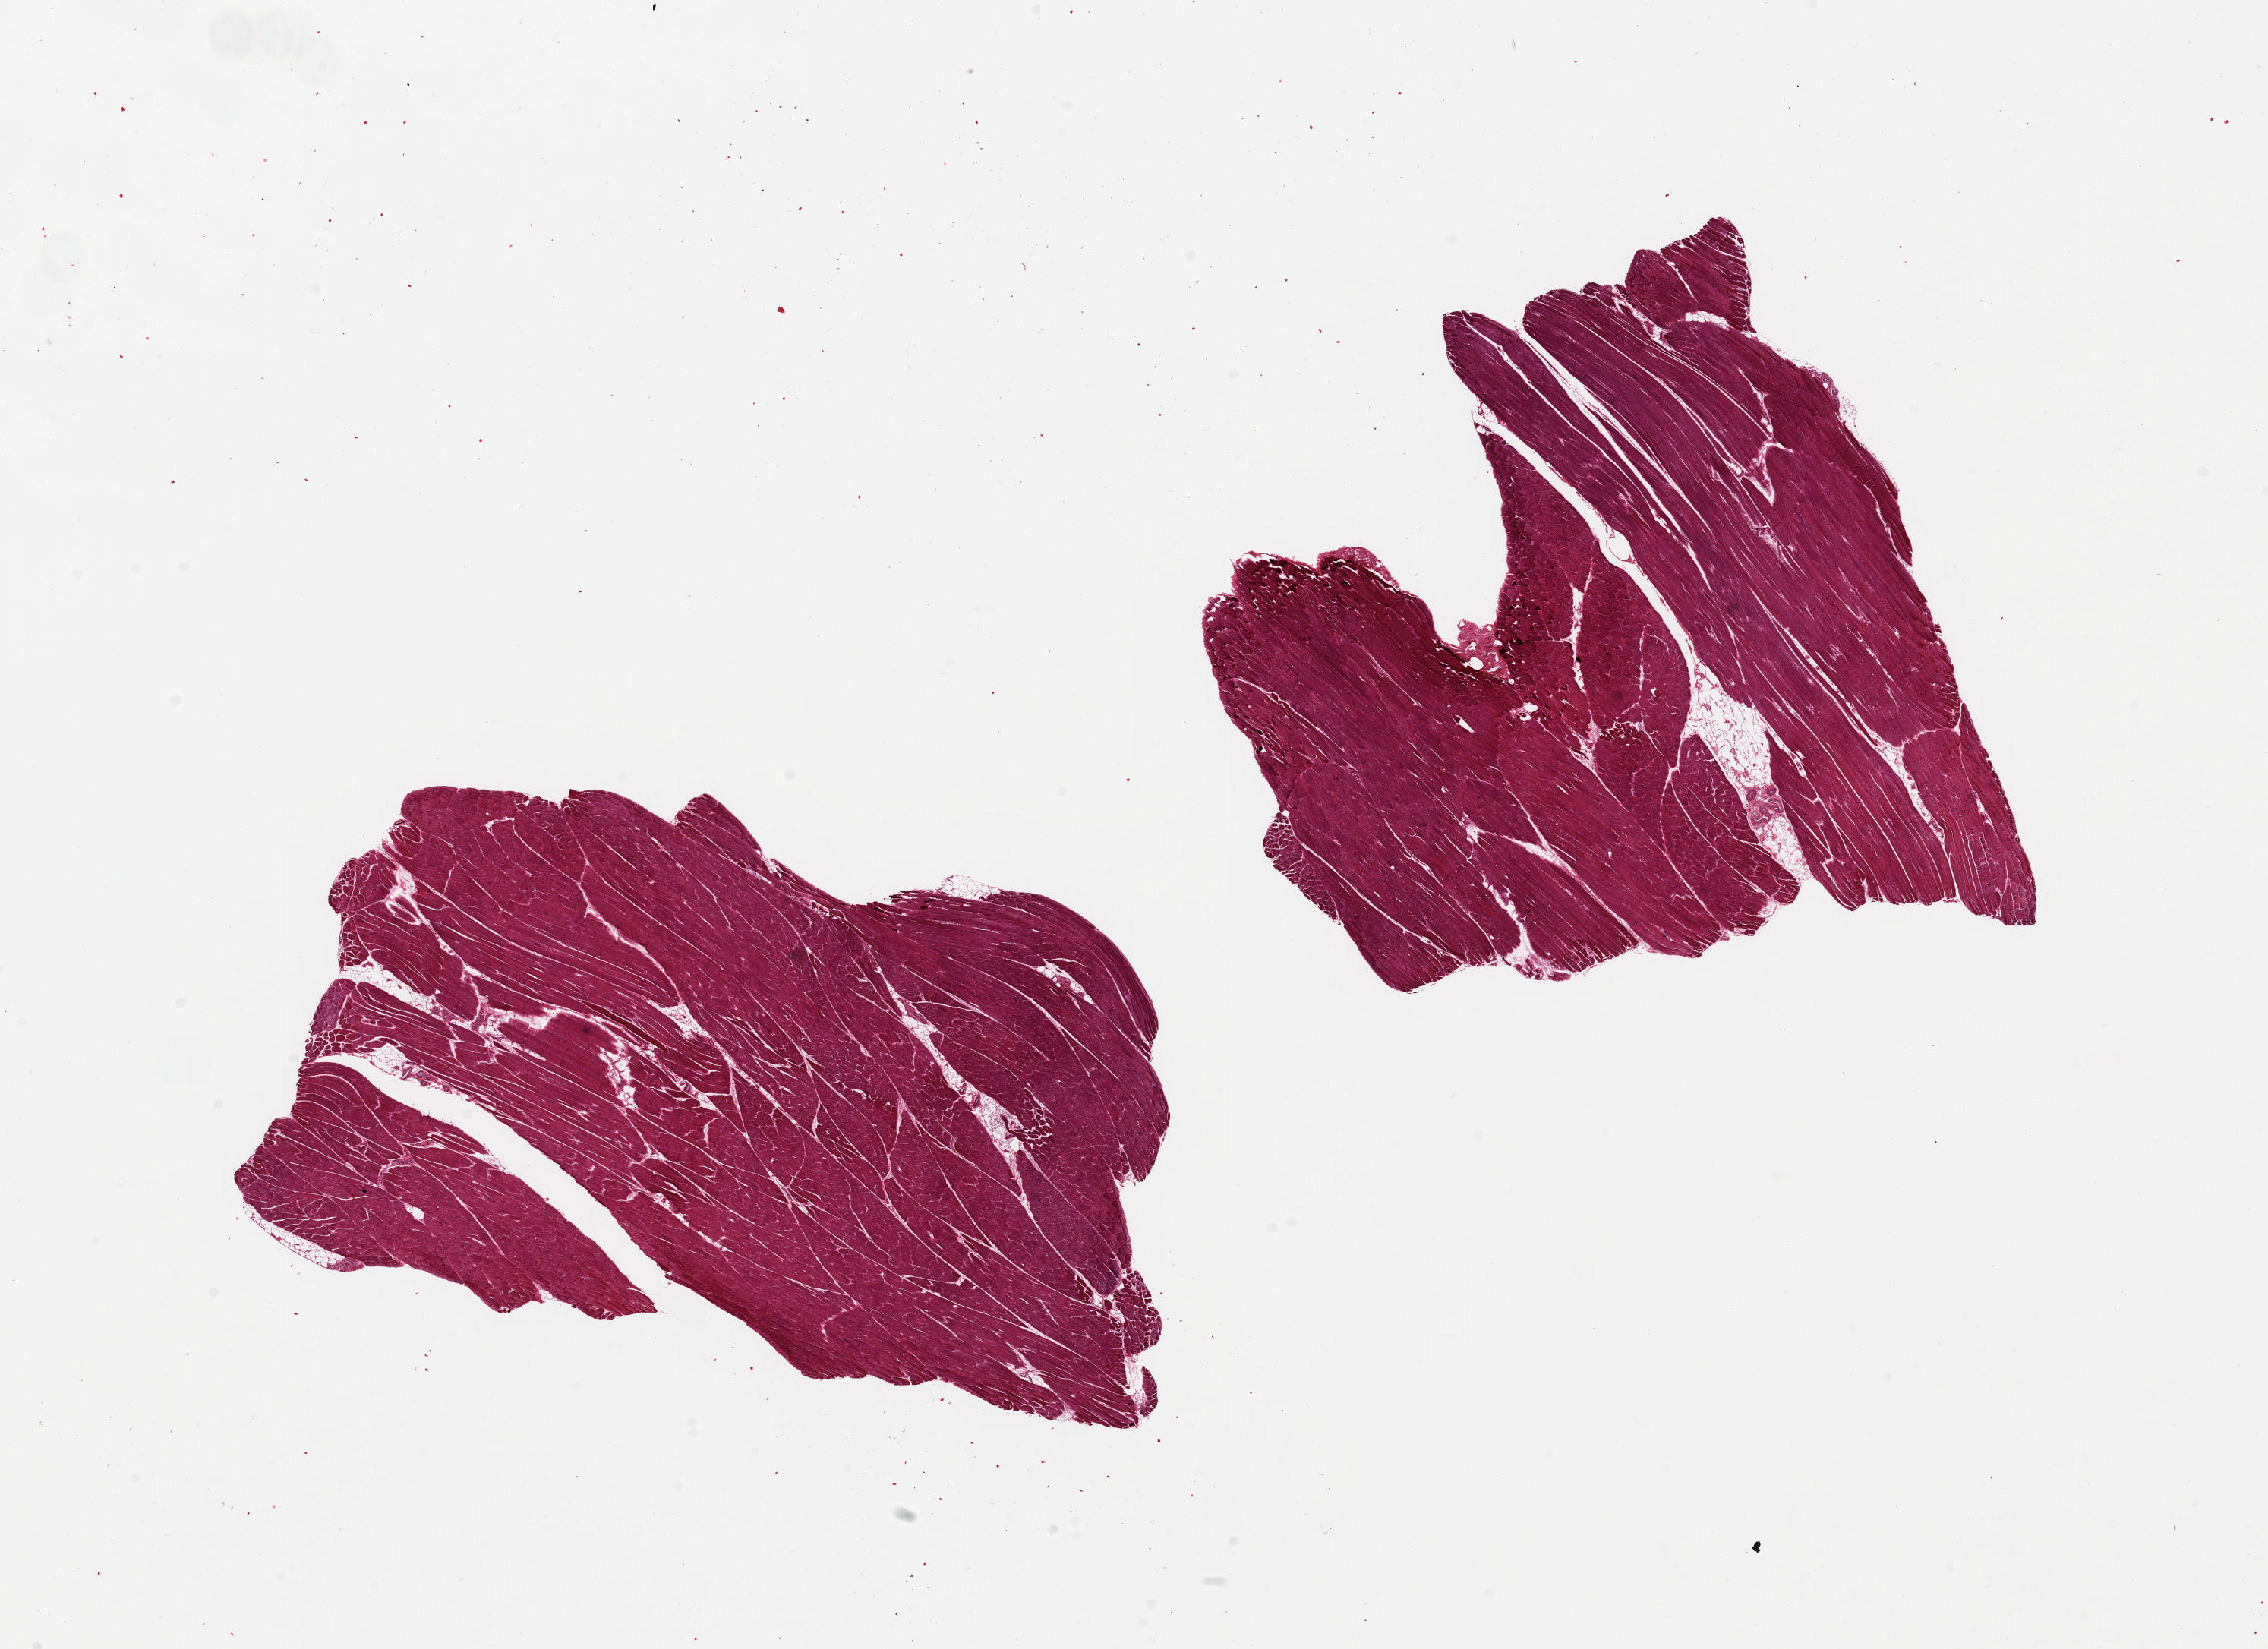
Digitized hematoxylin and eosin (H&E)-stained section, brightfield, shown as a low-resolution overview of the whole scanned area (about 23.6 x 17.2 mm, acquisition: 20x scan), PAXgene-fixed paraffin-embedded (PFPE) section, sampled site (target tissue): skeletal muscle, donor tissue sample. Donor sex: female.
Pathologist's review note for this sample: 2 pieces, minimal internal fat.